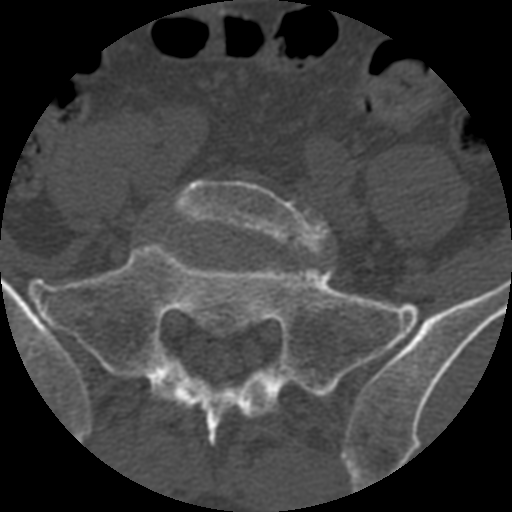
CT including the spine, one axial slice. Position 238 of 399 along the scan axis. 120 kVp. Bone window (W 1800 / L 400 HU). 512 × 512 image matrix. Patient age 71 years. Case-level facts recorded for this patient, not image findings: primary cancer: prostate.
Annotated regions visible in this slice (semi-automatically segmented with operator editing):
- L5 vertebra: box from (x=169, y=179) to (x=330, y=254) px